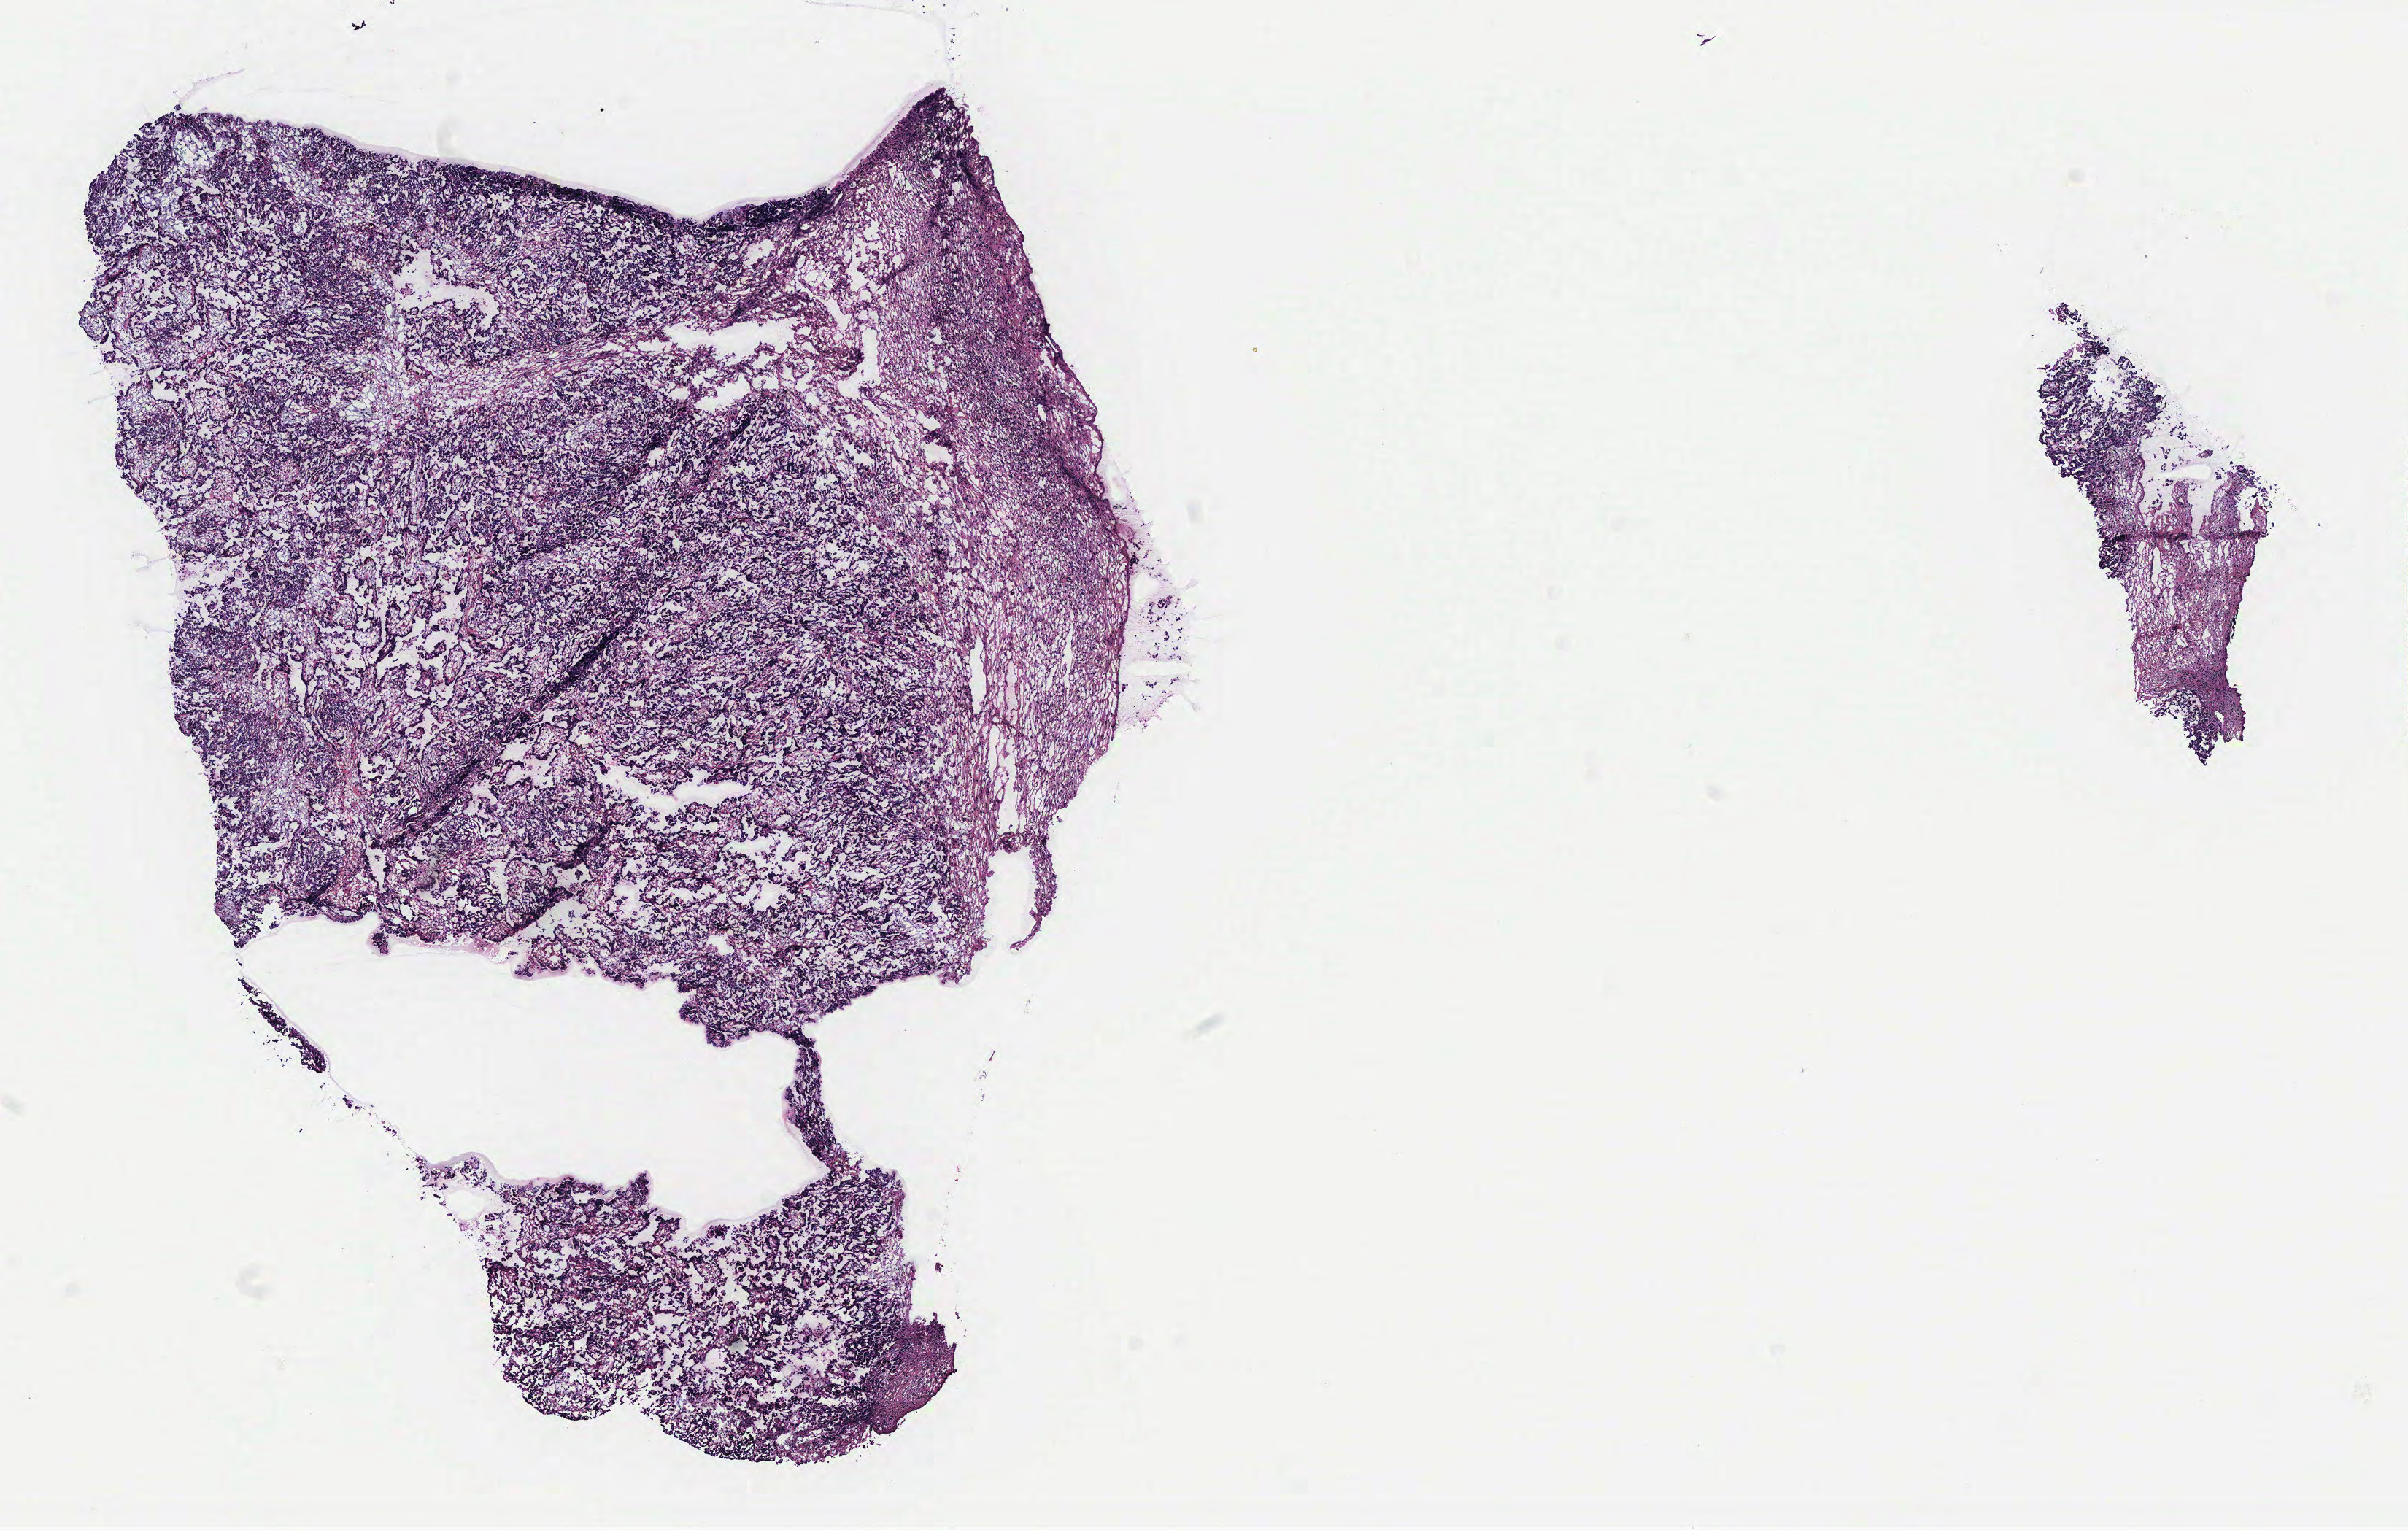
Whole-slide histology image, Hematoxylin and eosin (H&E) stained — low-resolution overview of the scanned area, about 13.2 x 8.4 mm (acquisition: 40x scan). Ovary, tumour tissue. 74-year-old female patient.
Primary tumour site (as recorded): peritoneum. Histologic diagnosis: Serous adenocarcinoma, NOS (peritoneum, NOS).